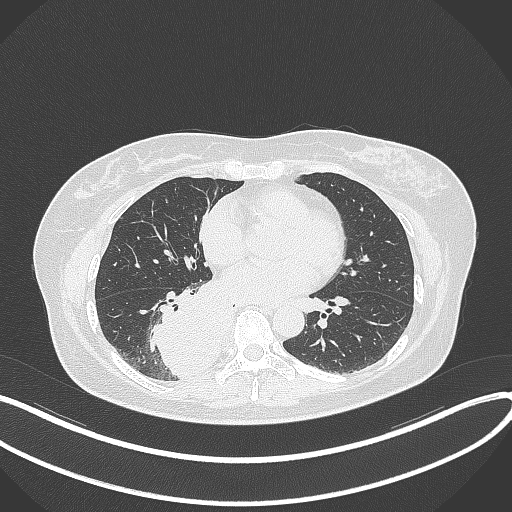
Chest CT, one axial slice; position 158 of 331 along the scan axis; lung window (W 1500 / L -600 HU); 1 mm slice thickness; 512 × 512 image matrix, field of view 400 × 400 mm. Female patient, age 54 years. From the clinical record (not read from this slice): clinical TNM (as recorded): T4 N0 M0.
Annotated regions visible in this slice (rectangle marked by the reading radiologist):
- lung tumour (recorded histology: adenocarcinoma): bounding box <149,286,229,381> (left, top, right, bottom; pixels)